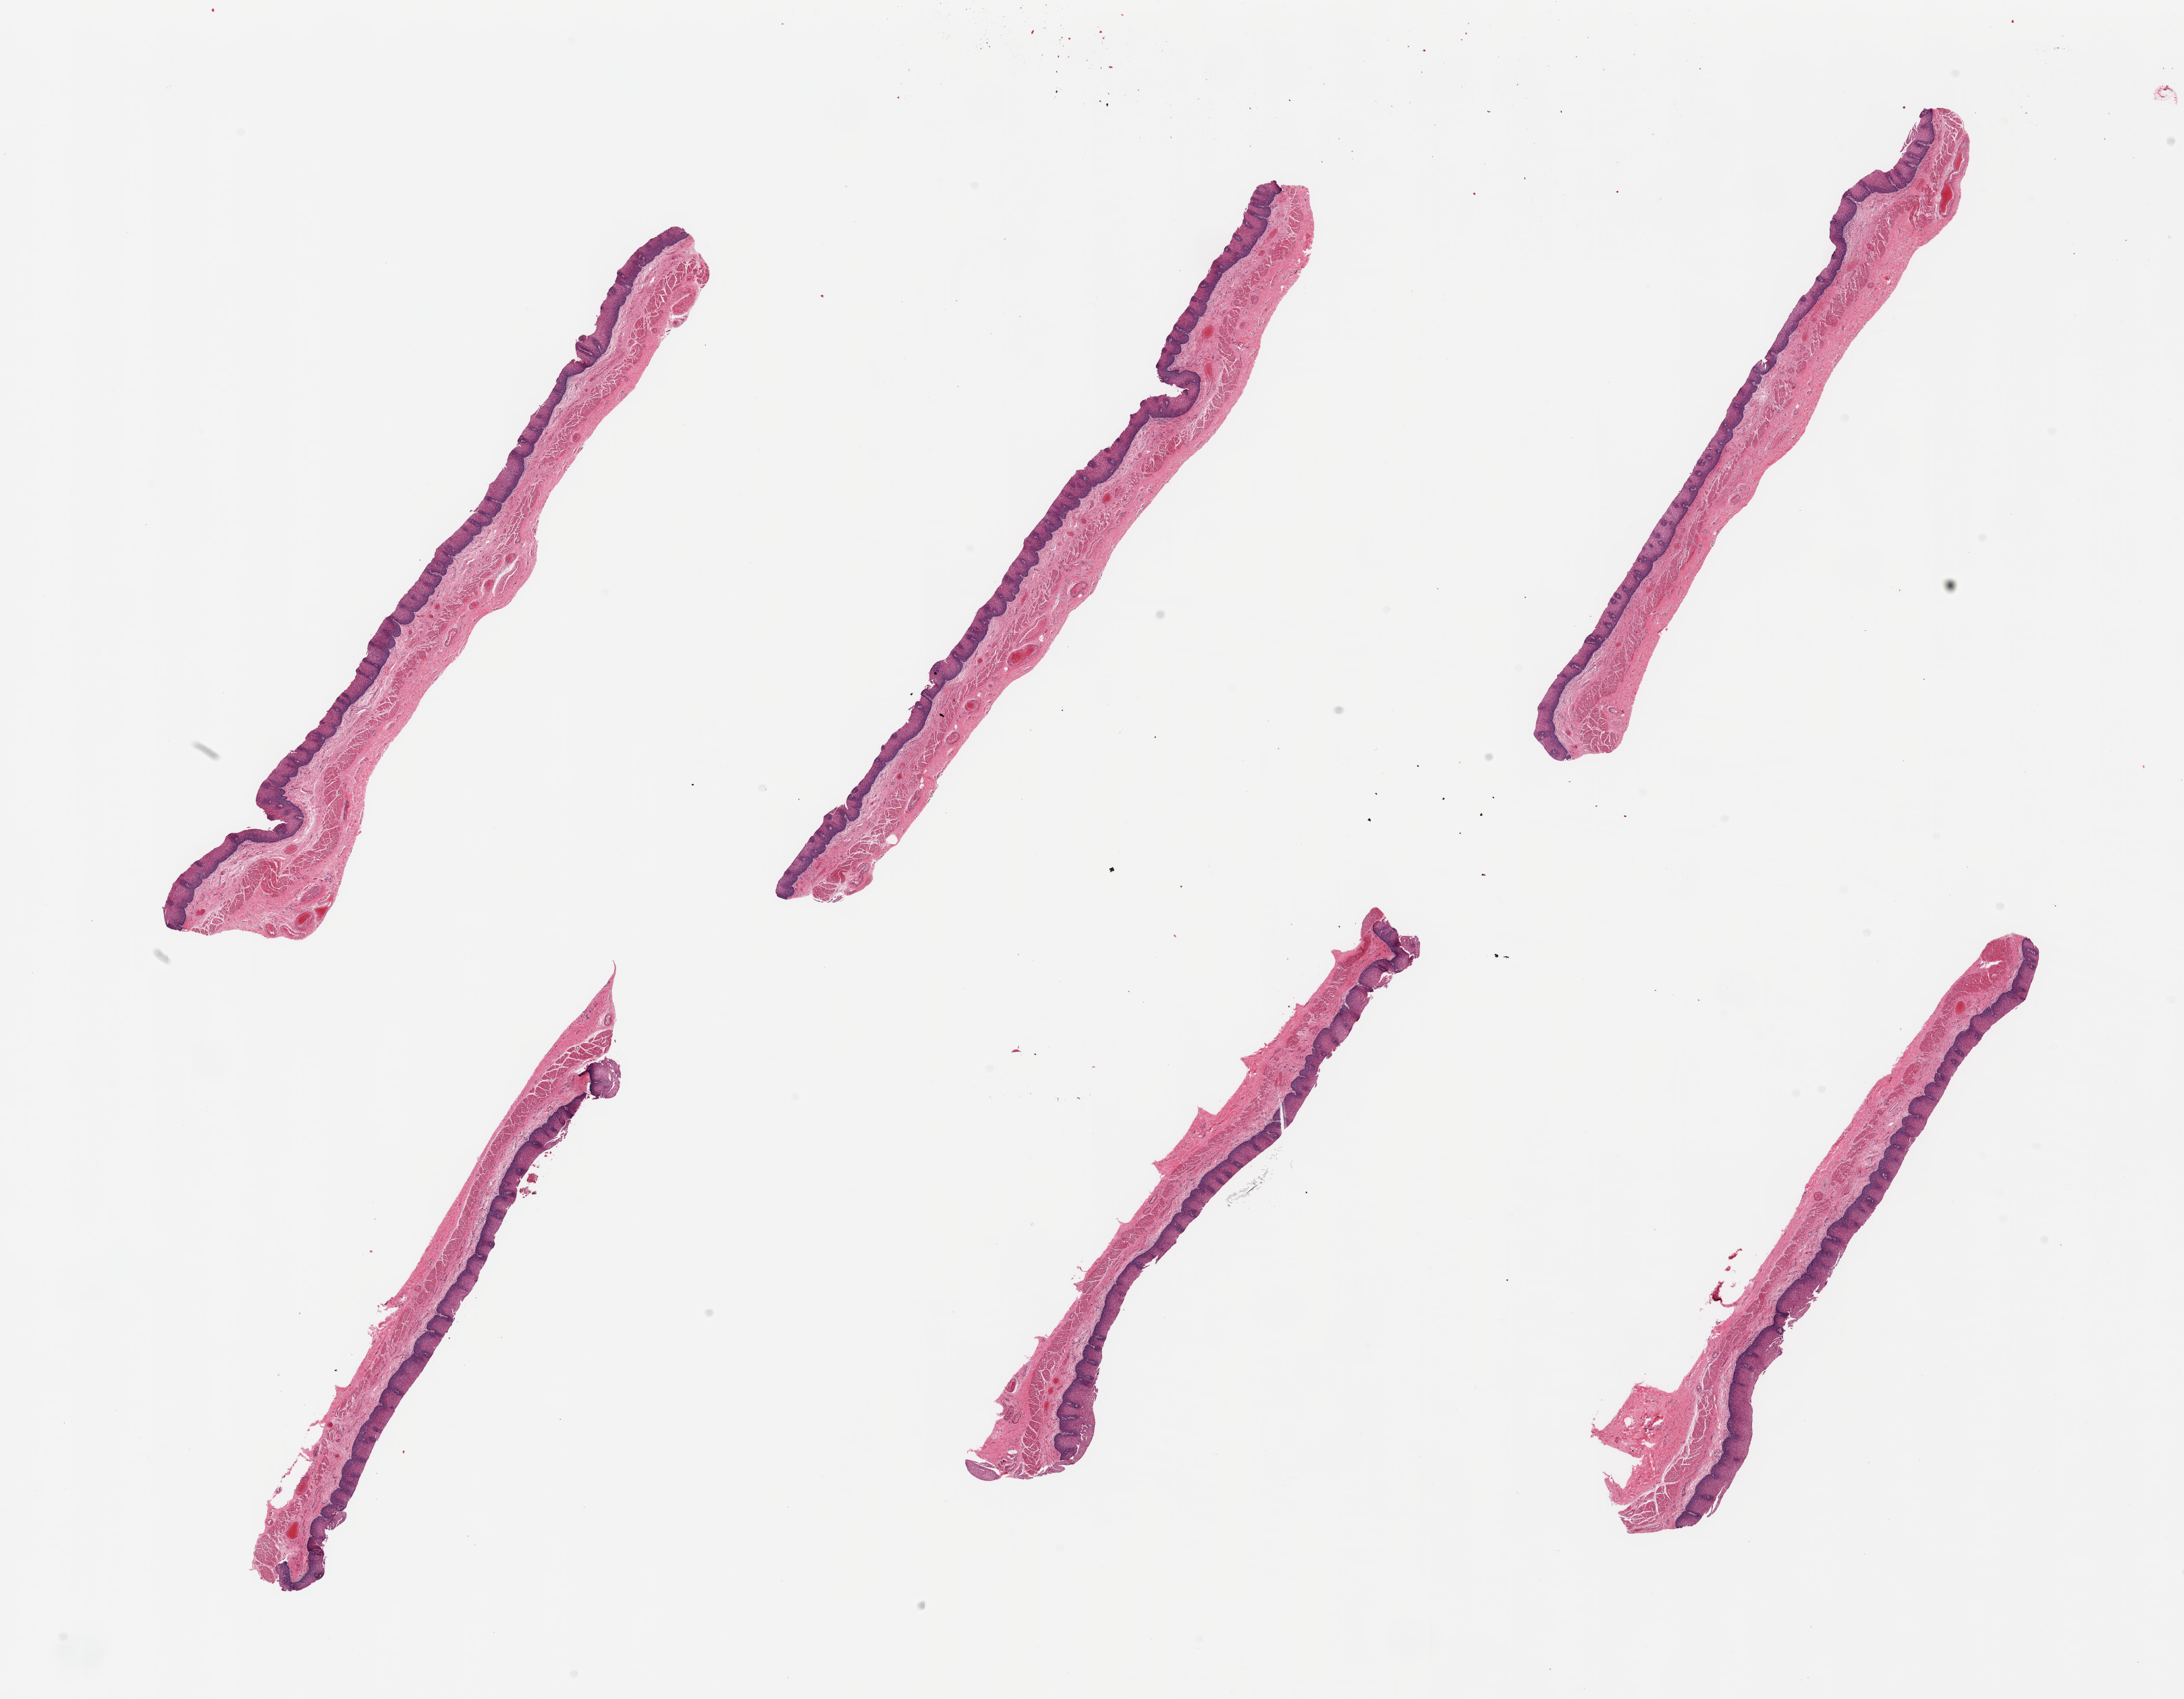
Whole-slide image, H&E stain, brightfield, shown as a low-resolution overview of the whole scanned area (about 25.6 x 19.9 mm, acquisition: 20x scan). PAXgene-fixed paraffin-embedded (PFPE) section. Sampled site (target tissue): esophageal mucous membrane. Donor tissue sample. Donor sex: male.
Review note (as recorded): 6 pieces; very superficial focal desquamation; ~0.25mm thick squamous epithelium.